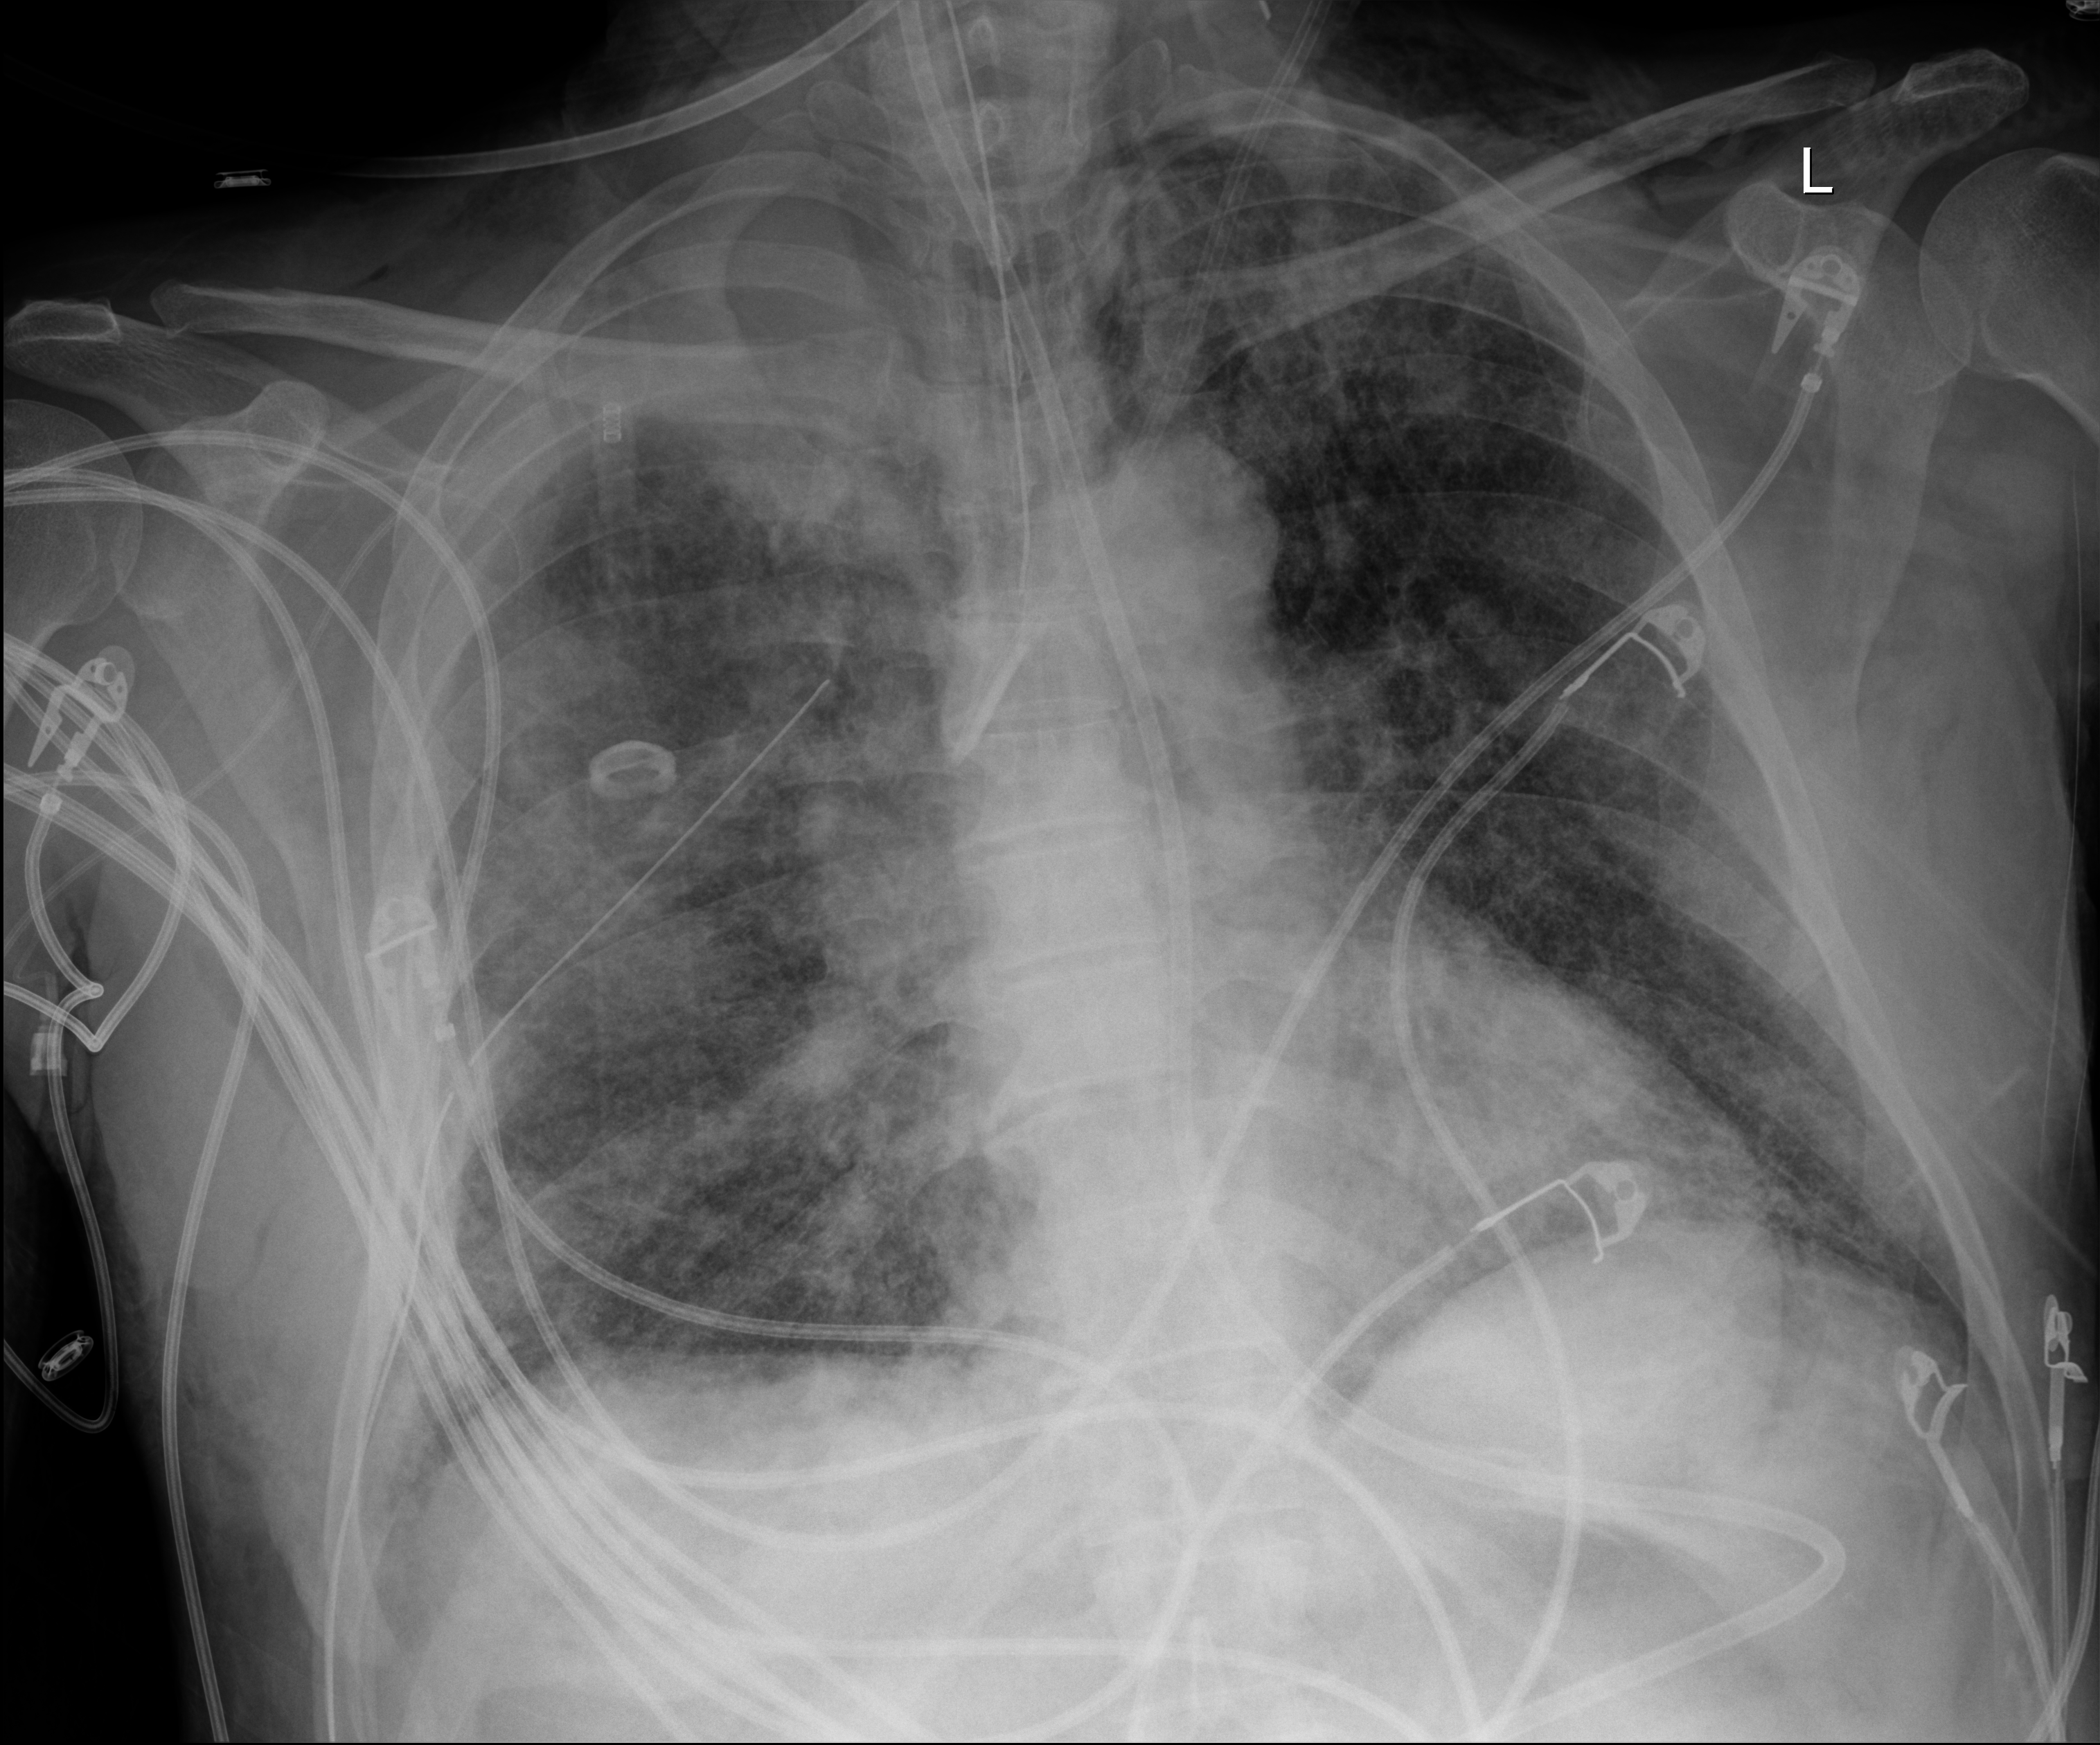
Bedside chest radiograph (digital radiography); anteroposterior (AP) projection. Patient hospitalised with COVID-19; male, aged 18–59 years.
Admission-level facts for this patient (not findings on this image; timing relative to this image not recorded):
- smoking status (admission record): never